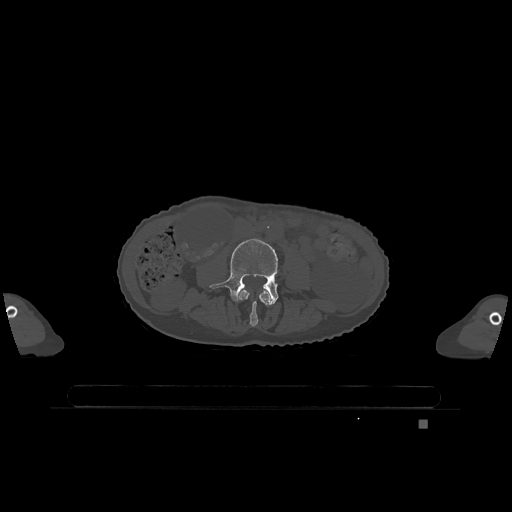
CT including the spine, one axial slice; position 317 of 1317 along the scan axis; bone window (W 1800 / L 400 HU); 0.5 mm slice thickness; 512 × 512 image matrix, field of view 500 × 500 mm. Patient: female, 74 years. Case-level facts recorded for this patient, not image findings: primary cancer: lung.
Outlined on this slice (semi-automatic segmentation, software-assisted and operator-edited):
- L3 vertebra: bounding box [x1, y1, x2, y2] px = [239, 289, 271, 327]
- L4 vertebra: [209, 239, 278, 305]